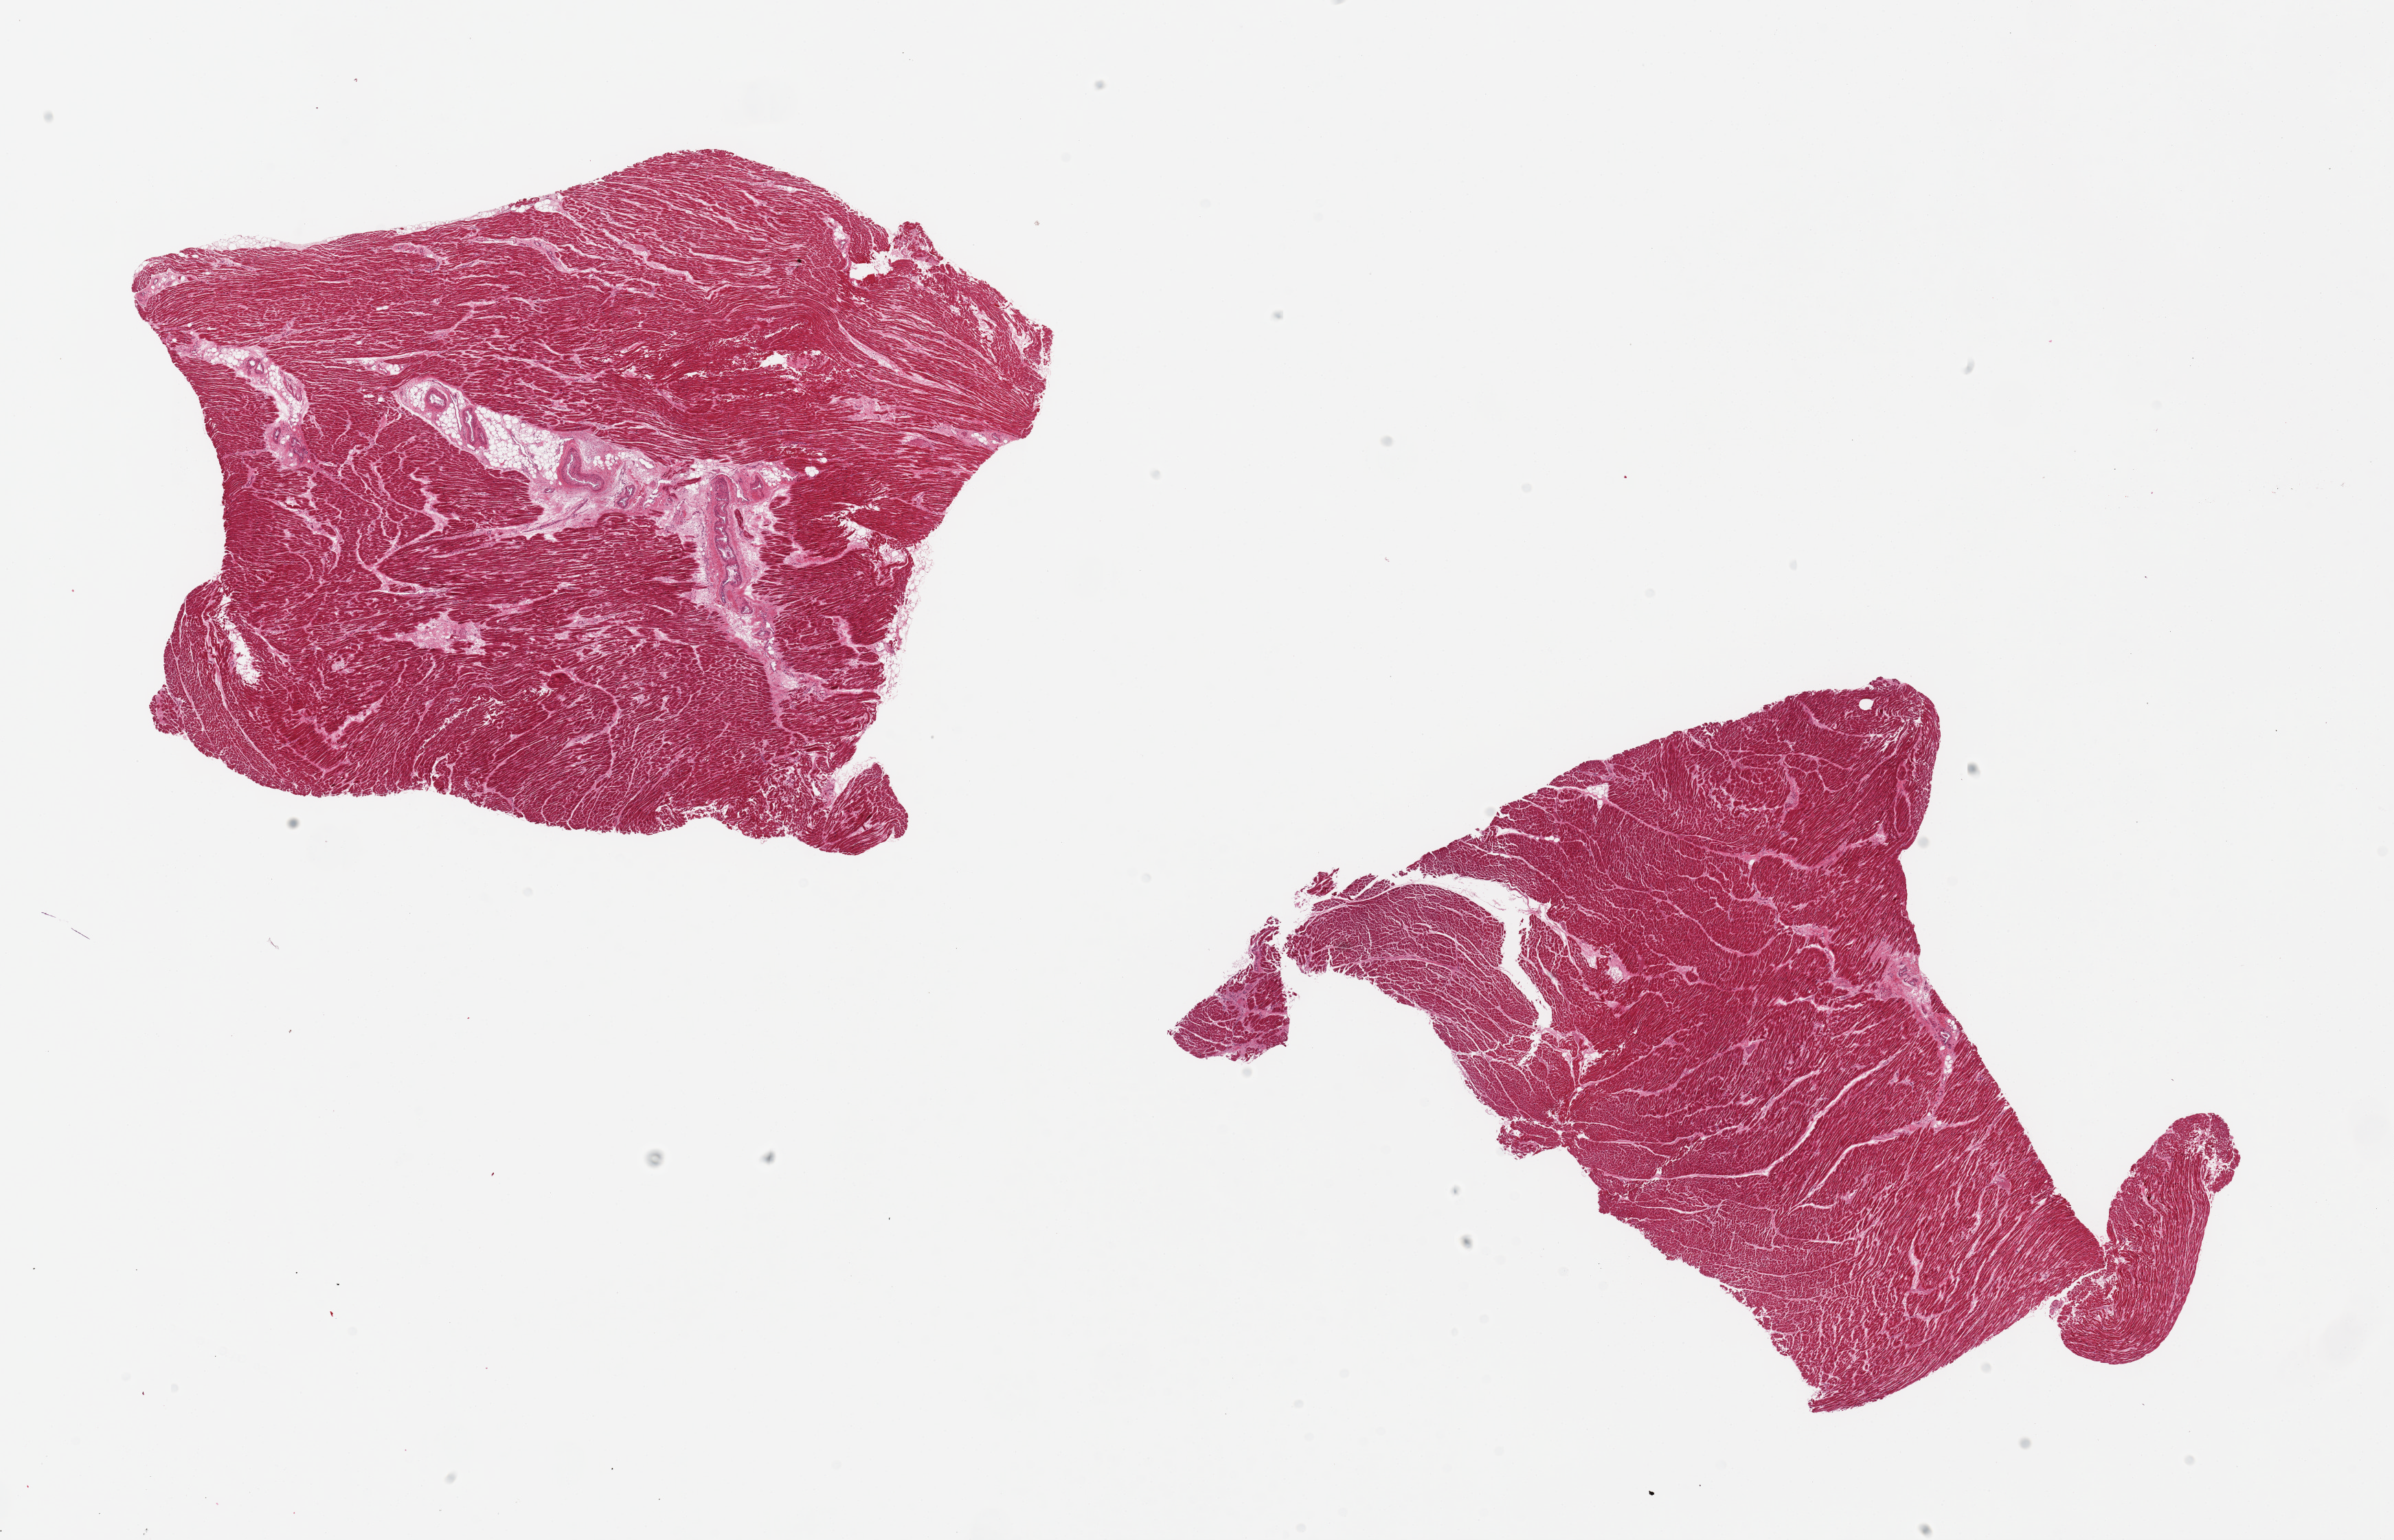
Whole-slide image, haematoxylin and eosin stain, brightfield, whole scanned area (about 27.6 x 17.7 mm, from a 20x scan) shown as a low-resolution overview, PAXgene-fixed, paraffin-embedded tissue, sampled site (target tissue): heart, tissue donor sample. Donor: male.
Reviewer comment on this tissue sample: 2 pieces.